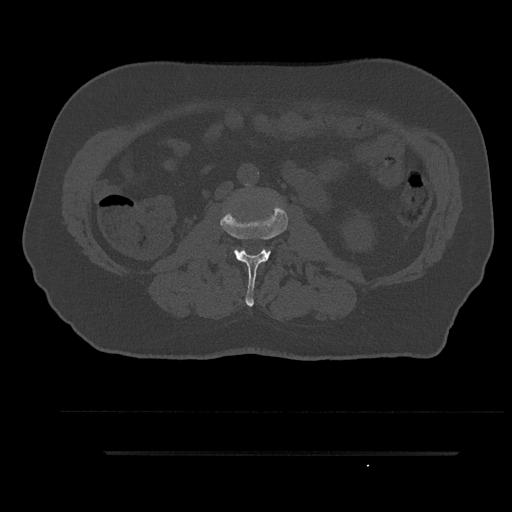
CT including the spine, one axial slice. Position 91 of 797 along the scan axis. Reconstruction kernel Br40s/3. Bone window (W 1800 / L 400 HU). 512 × 512 image matrix, field of view 432 × 432 mm. Male patient, age 63 years. From the clinical record (not read from this slice): primary cancer: renal.
Annotated regions visible in this slice (semi-automatically segmented with operator editing):
- L2 vertebra: bounding box [x1, y1, x2, y2] px = [220, 205, 288, 307]